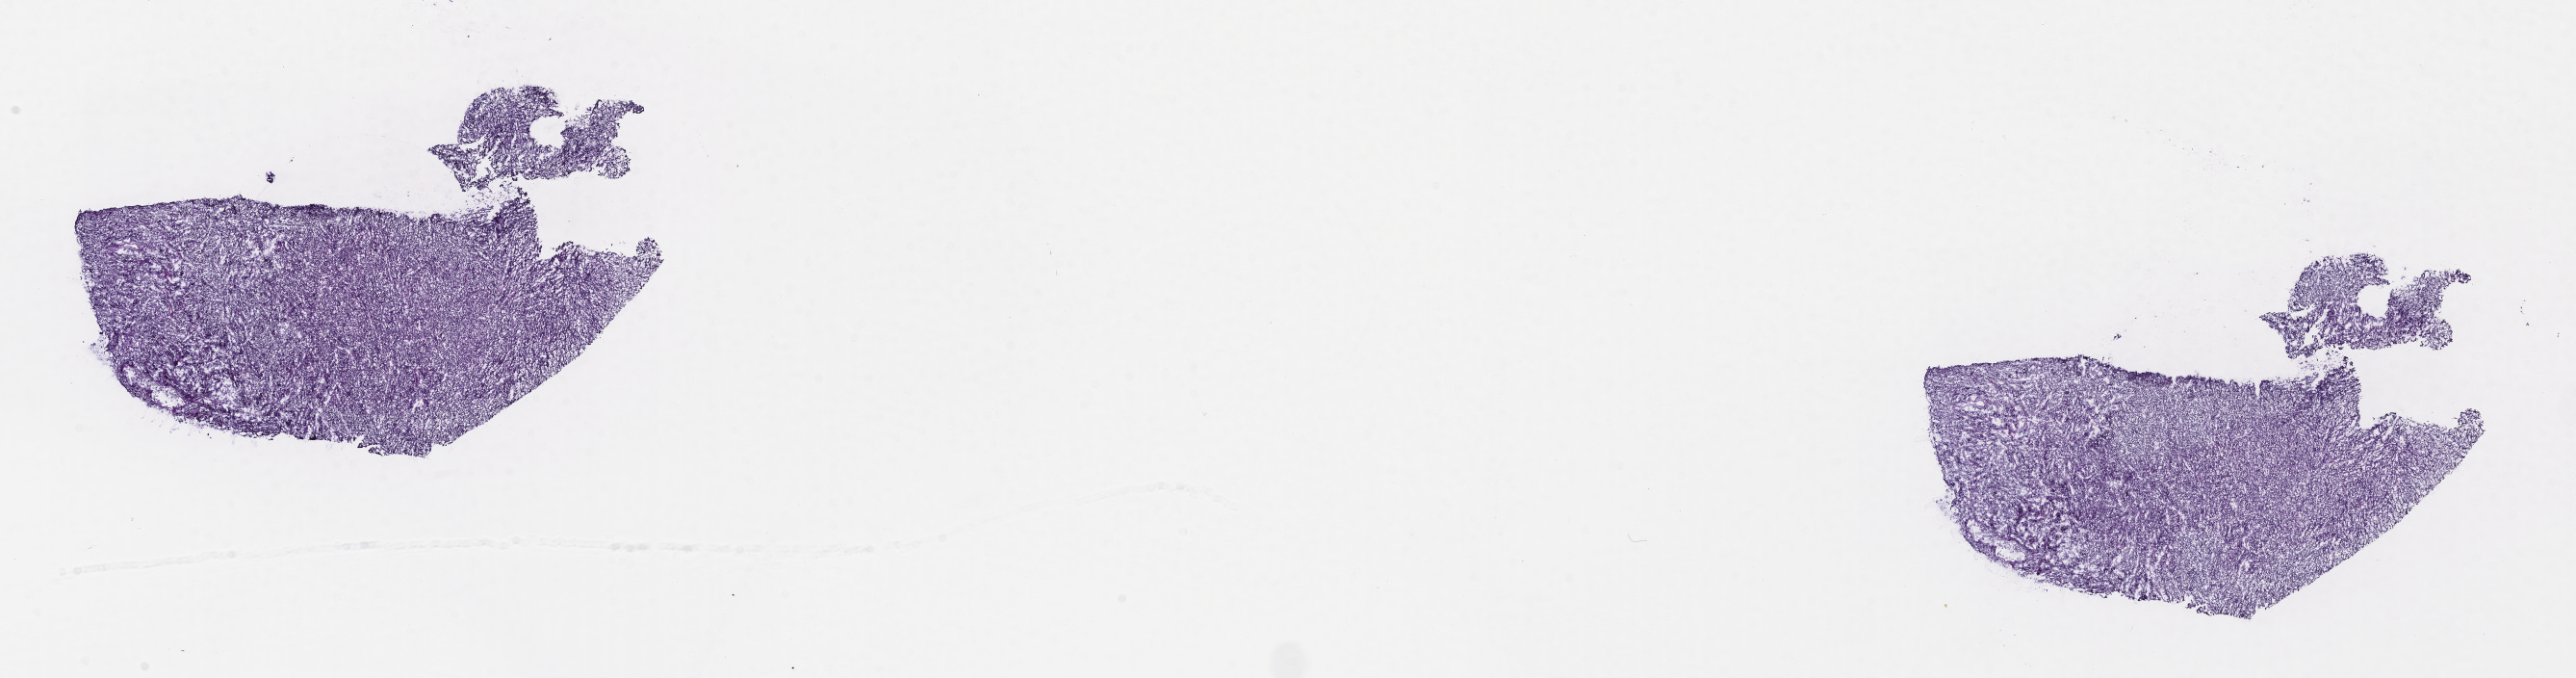
Whole-slide image, H&E stain — low-resolution overview of the scanned area, about 21.6 x 5.7 mm; frozen section; specimen: primary tumor; site: retroperitoneum. Patient: male, age at initial diagnosis 7 years. Composition of this section per pathologist review: tumor cells 90%, tumor nuclei 95%, stromal cells 5%, necrosis 0%, normal cells 5%. Infiltration values recorded for this section: lymphocyte infiltration 80%, monocyte infiltration 15%, neutrophil infiltration 0%.
Histologic diagnosis: Diffuse large B-cell lymphoma, NOS. Section: bottom of the tissue portion. Ann Arbor stage (patient): Stage IV.